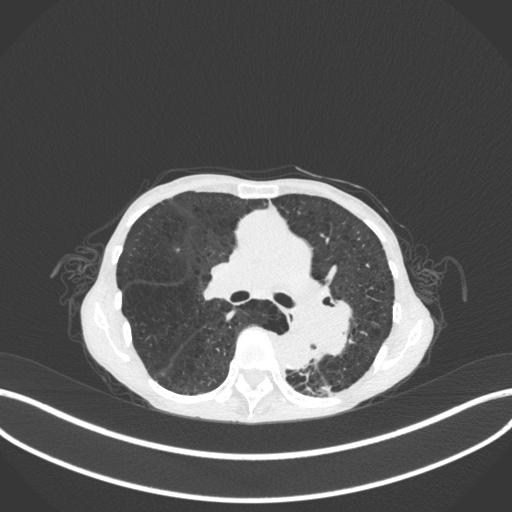
Chest CT, one axial slice. Reconstruction kernel B31f. Lung window (W 1500 / L -600 HU). 1 mm slice thickness. 512 × 512 image matrix. Female patient, age 70 years. From the clinical record (not read from this slice): clinical TNM (as recorded): T3 N0 M0.
Annotated regions visible in this slice (rectangle marked by the reading radiologist):
- lung tumour (recorded histology: small cell carcinoma): bounding box <307,279,357,365> (left, top, right, bottom; pixels)